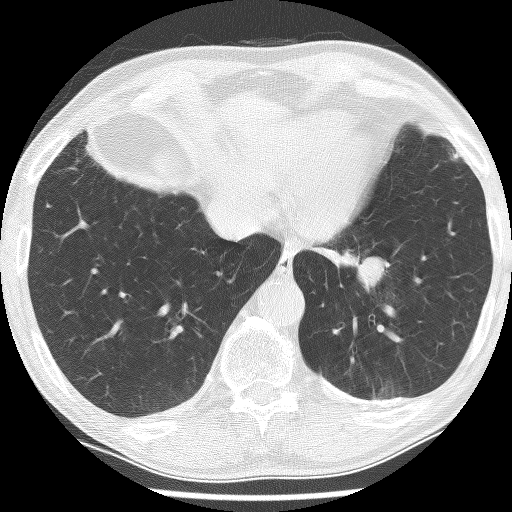
Low-dose screening chest CT, one axial slice. Position 41 of 226 along the scan axis. Reconstruction kernel BONE. Lung window (W 1500 / L -600 HU). 512 × 512 image matrix.
Annotated regions visible in this slice (expert manual segmentation):
- lesion 1 (tumor, lower lobe of left lung): bounding box [x1, y1, x2, y2] px = [343, 250, 384, 293]